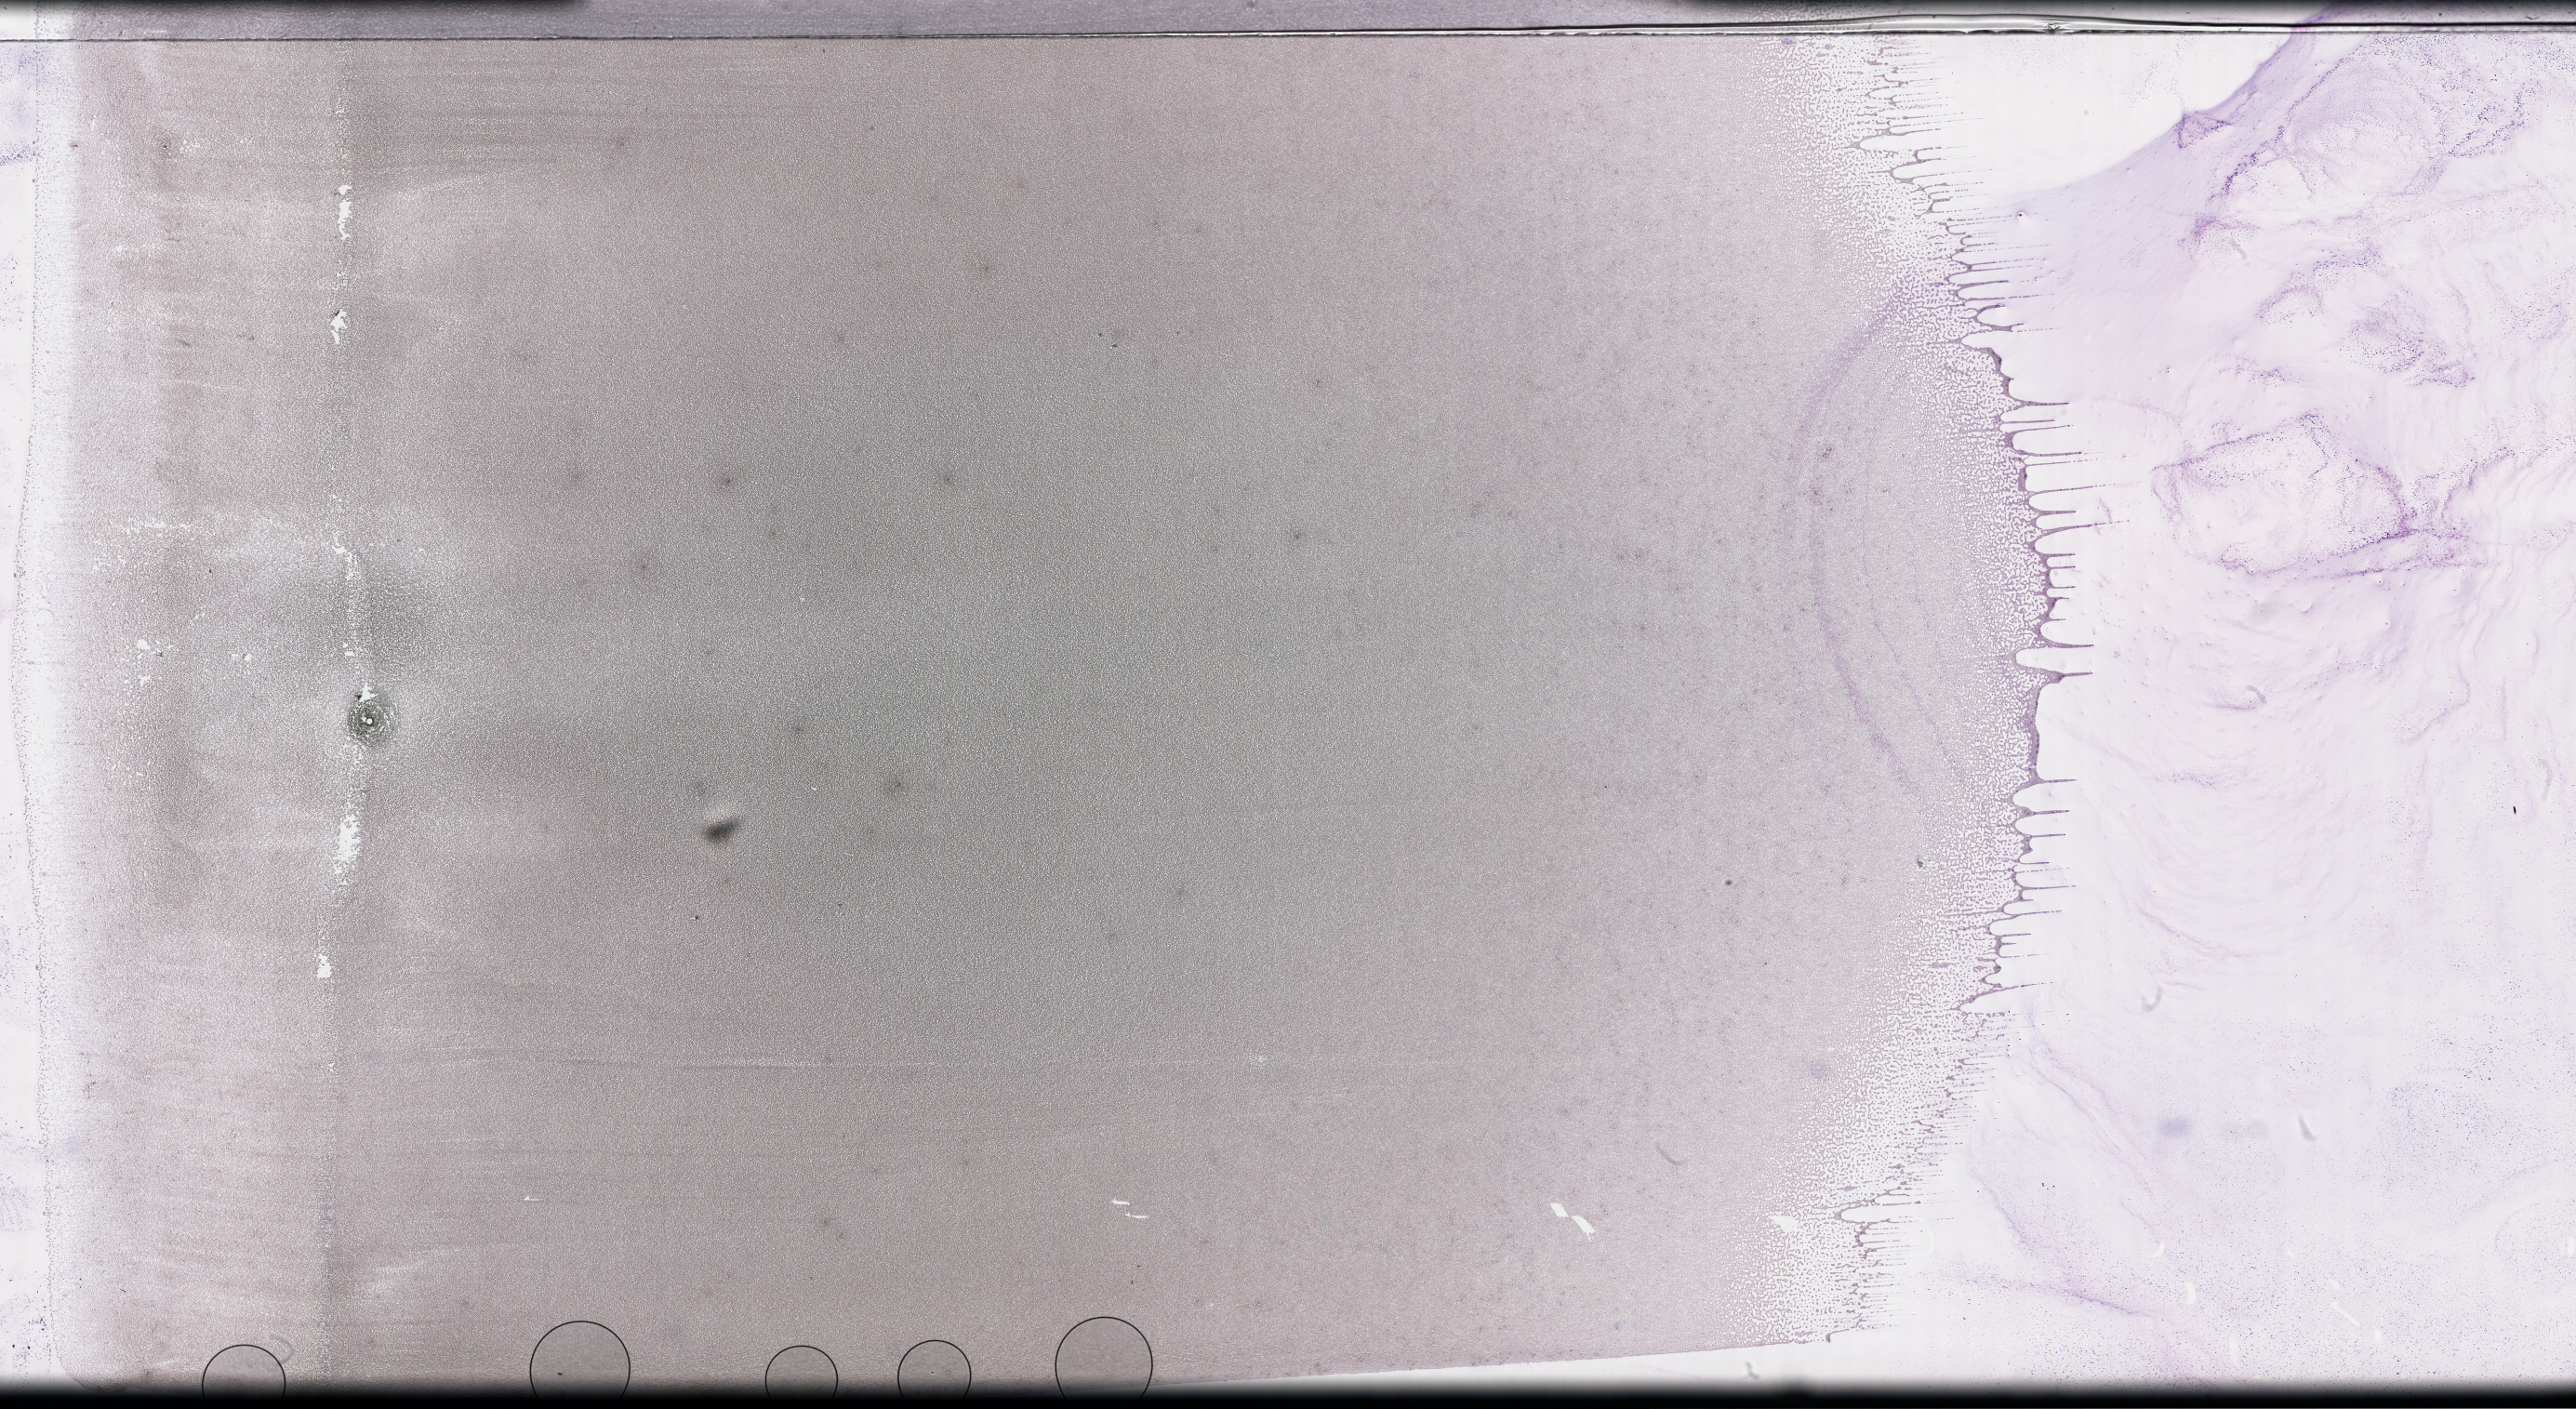
Wright–Giemsa-stained whole blood smear, whole-slide image — low-resolution overview of the scanned area, about 44.7 x 24.5 mm. Patient: female.
• from a patient with: Plasma Cell Myeloma